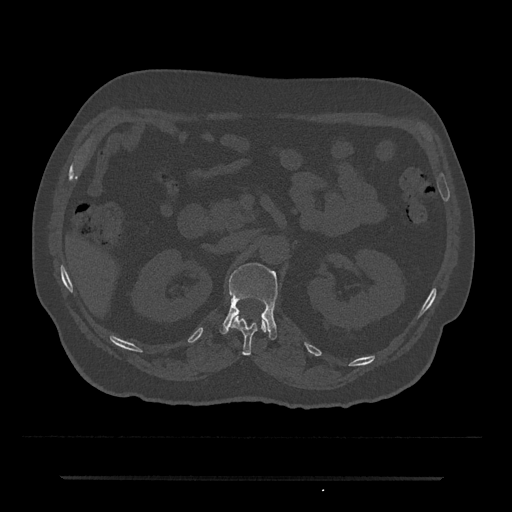
CT including the spine, one axial slice; slice 94 of 797 in the series (ordered by position); bone window (W 1800 / L 400 HU); 0.5 mm slice thickness; 512 × 512 image matrix, field of view 437 × 437 mm. Male patient, age 69 years. From the clinical record (not read from this slice): primary cancer: prostate.
Annotated regions visible in this slice (semi-automatic segmentation, software-assisted and operator-edited):
- L1 vertebra: bounding box [x1, y1, x2, y2] px = [219, 263, 278, 340]
- T12 vertebra: [231, 314, 268, 356]